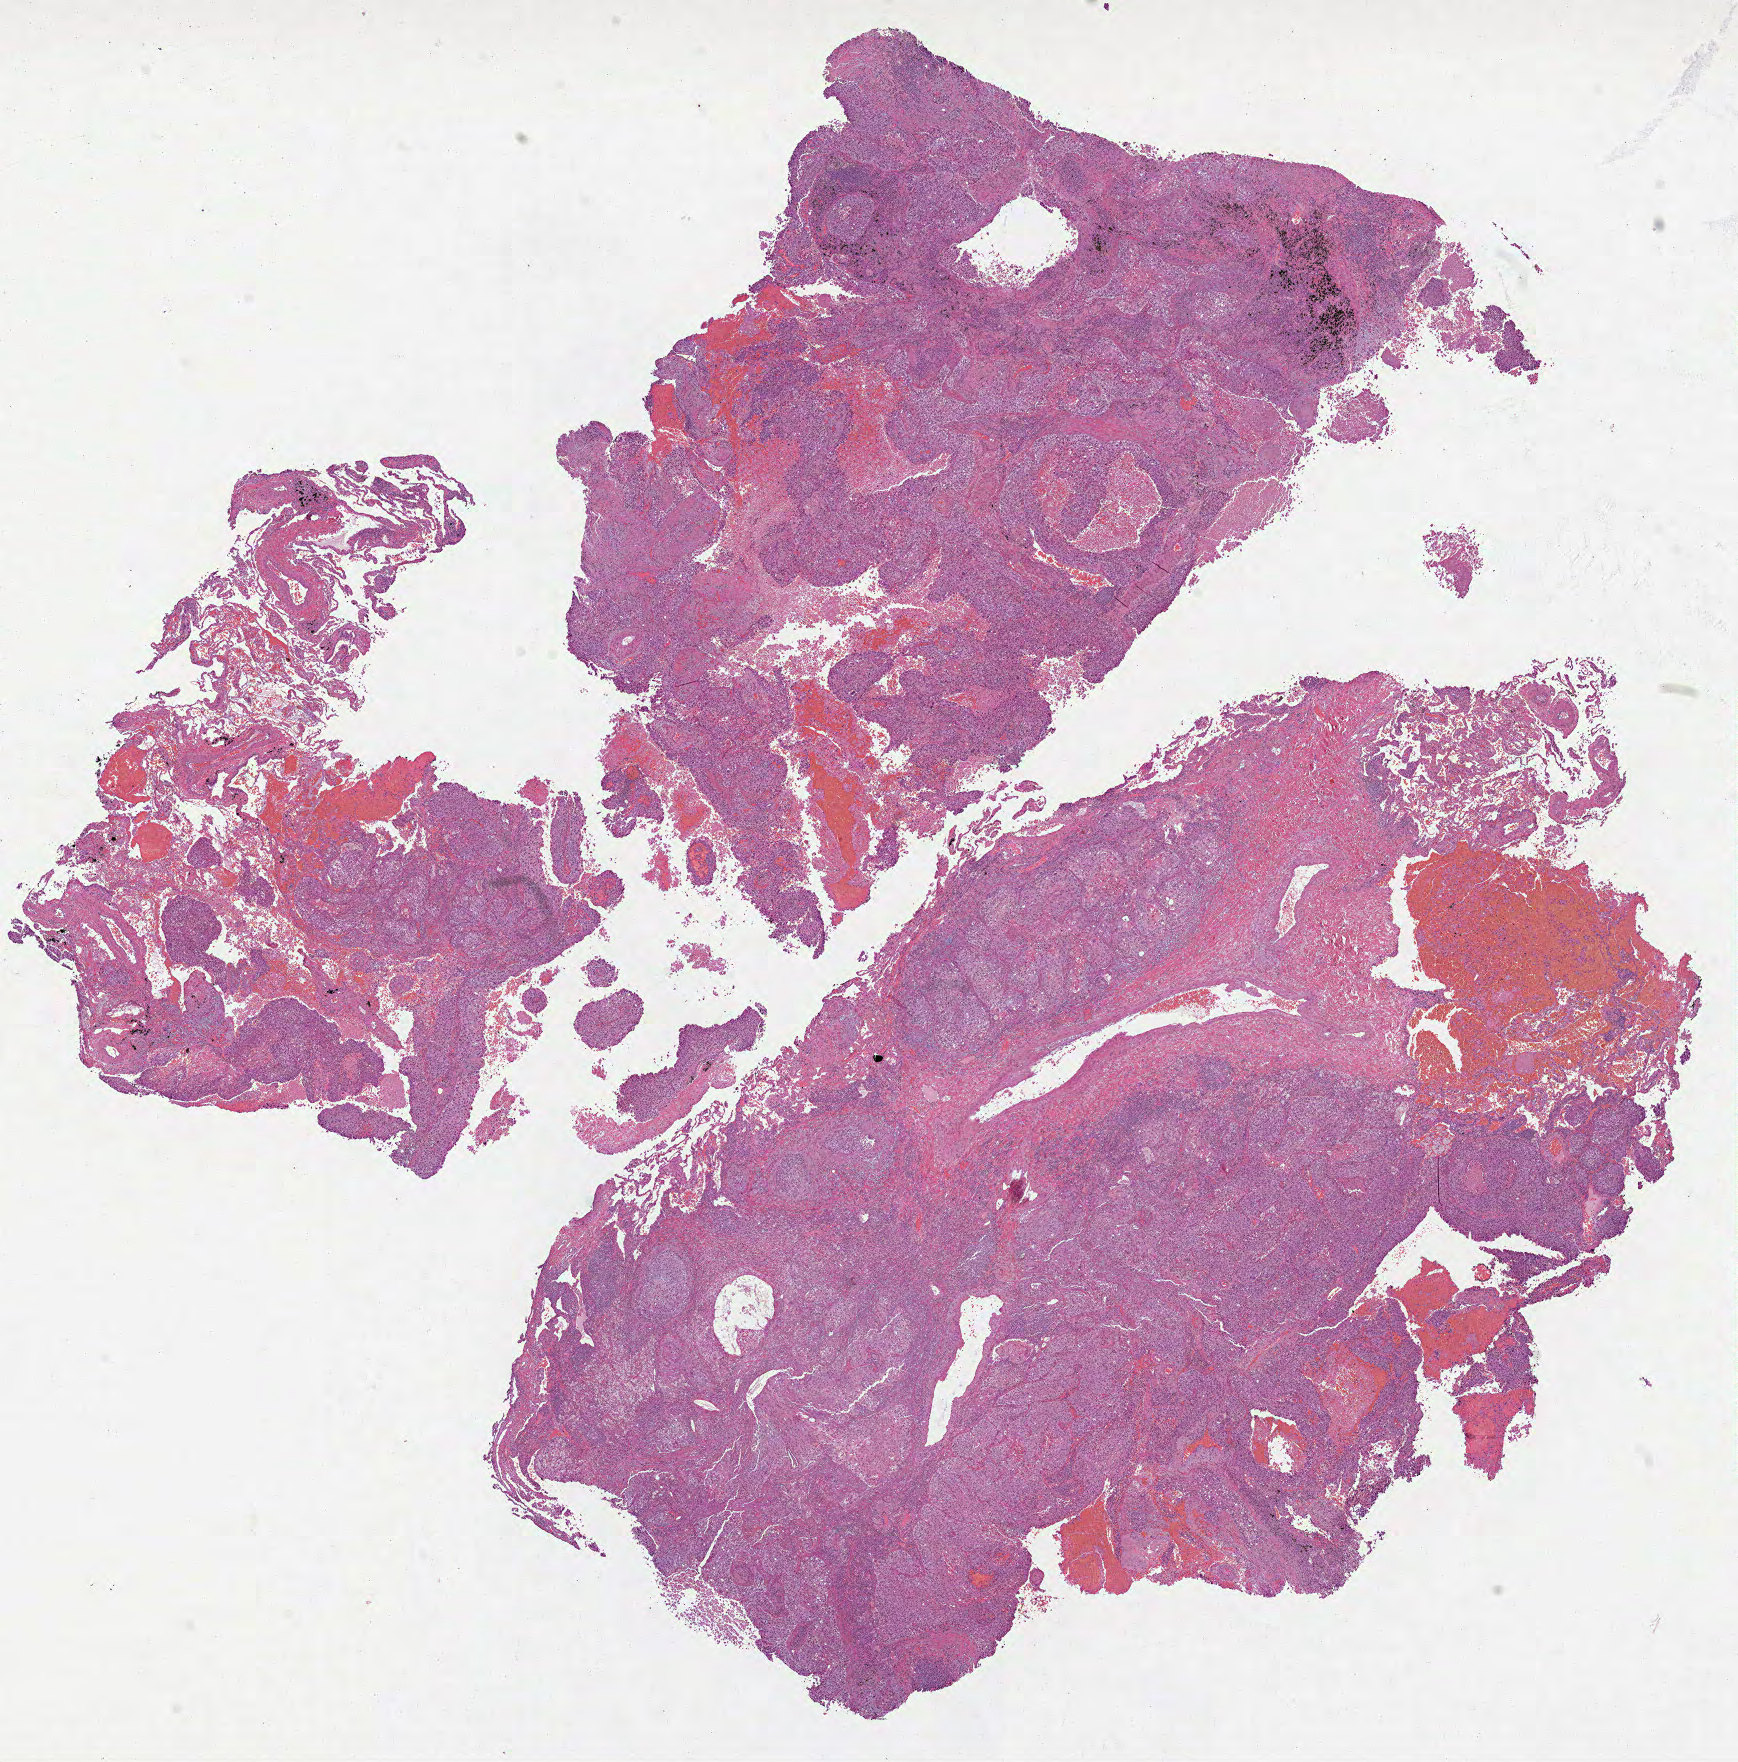
Digitized H&E-stained tissue section (whole slide), shown as a low-resolution overview of the whole scanned area (about 14.0 x 14.2 mm, from a 40x scan). Formalin-fixed paraffin-embedded (FFPE) diagnostic section. Primary tumour sample from the lung. Patient: male, age at initial diagnosis 66 years.
• diagnosis: Squamous cell carcinoma, keratinizing, NOS (upper lobe, lung)
• AJCC pathologic stage: IB